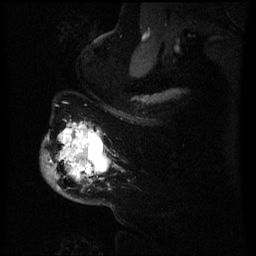
Breast MRI (dynamic contrast-enhanced), one sagittal slice. Position 48 of 60 along the scan axis. Dynamic contrast-enhanced series, image 2 of 3 at this slice position (ordered by acquisition). 1.5 T. TE 4.2 ms, TR 8 ms. 256 × 256 image matrix. Female patient, age 50 years.
Outlined on this slice (semi-automatically segmented with operator editing):
- analysis volume of interest (the breast-tissue region the enhancement analysis was run in; not a lesion): bounding box (x1, y1, x2, y2) in pixels: (47, 122, 110, 191)
- tumour enhancement mask (voxels above the 70 % enhancement threshold inside the analysis volume of interest): (65, 126, 101, 173)